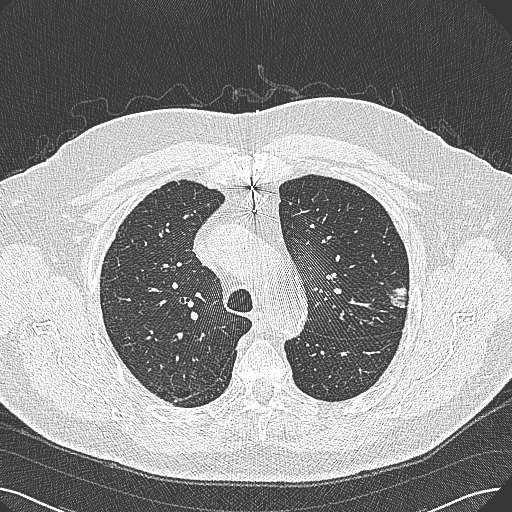
Chest CT (low-dose screening protocol), one axial image; first (baseline) screen; lung window (W 1500 / L -600 HU); 1 mm slice thickness; lung (sharp) reconstruction kernel (B80f); slice 74 of 269 in the series. Male participant, aged 74 years at enrolment.
Lesion marked by an expert reader, bounding box [x1, y1, x2, y2] px = [376, 273, 422, 317]. The exam's reader record, not a measurement of the box and not confirmed to be the same lesion: non-calcified nodule or mass ≥4 mm, left upper lobe, 15 × 10 mm, poorly defined margins, soft tissue attenuation. Official screen result: positive, change unspecified: nodule(s) >= 4 mm or enlarging nodule(s), mass(es), or other non-specific abnormalities suspicious for lung cancer.